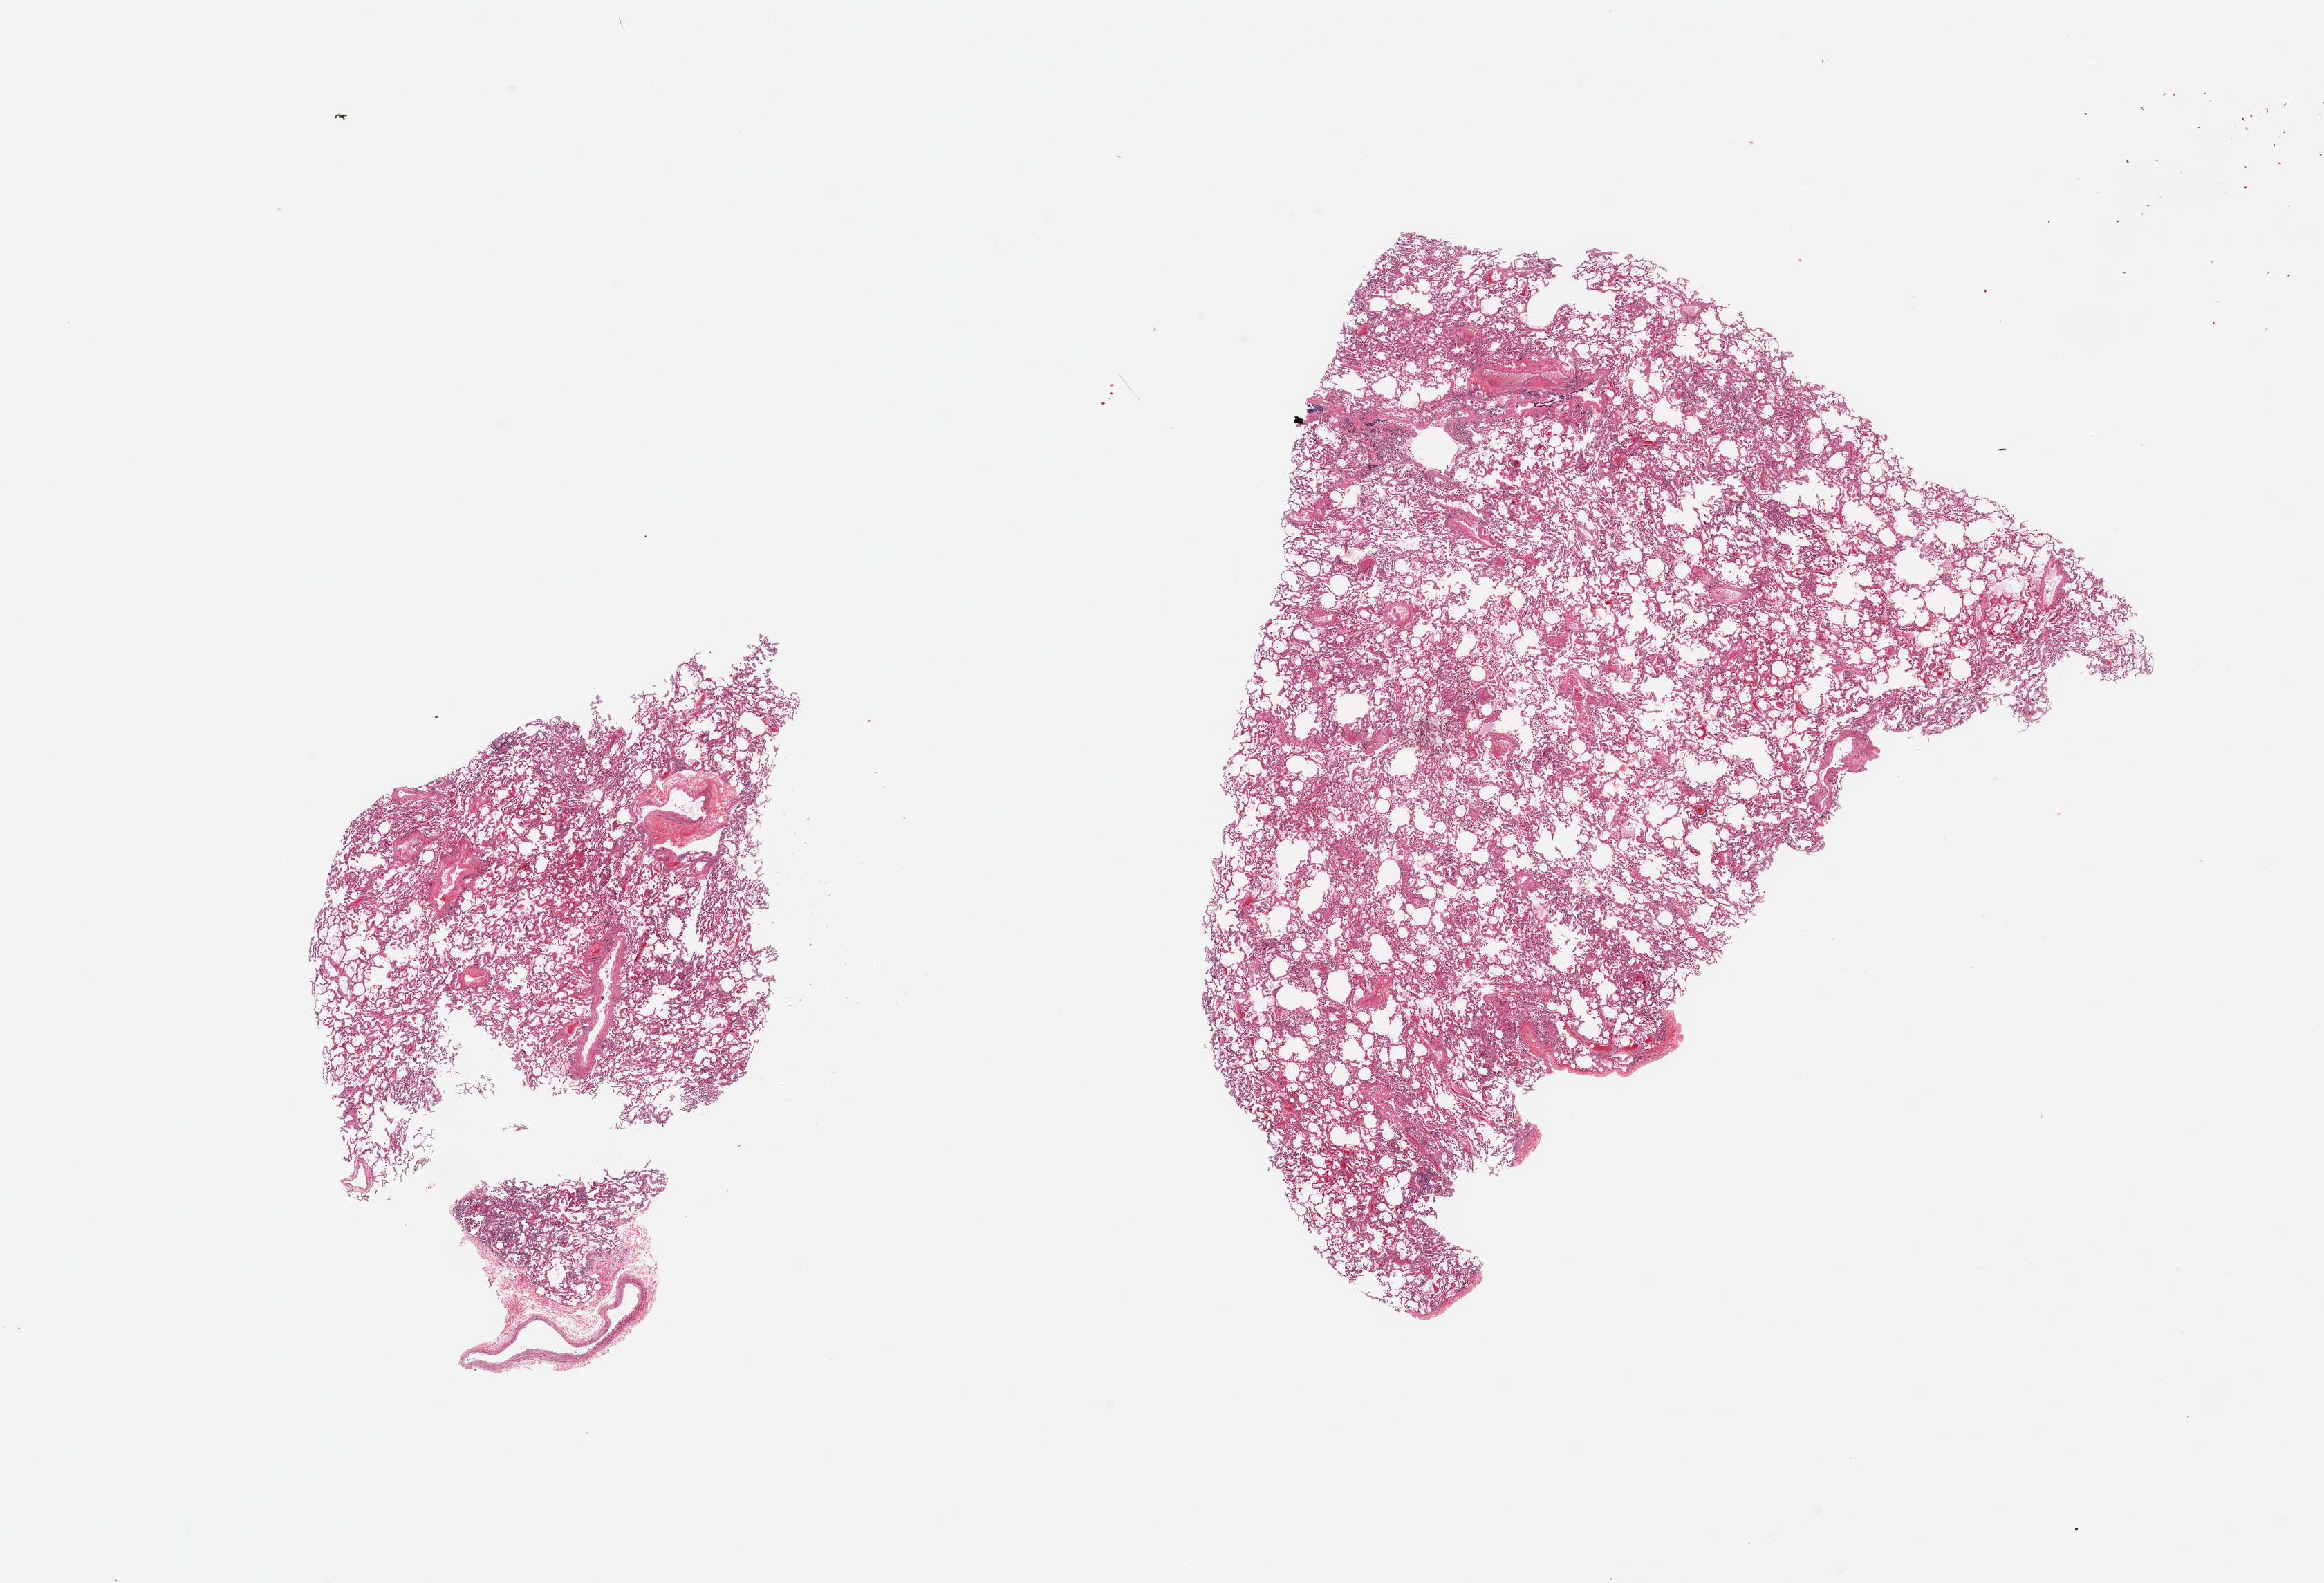
Whole-slide image, H&E stain — low-resolution overview of the scanned area, about 26.6 x 18.1 mm. PAXgene-fixed, paraffin-embedded tissue. Section of lung (target tissue). Tissue donor sample. Donor: male.
Reviewer comment on this tissue sample: 2 pieces, mild congestion.